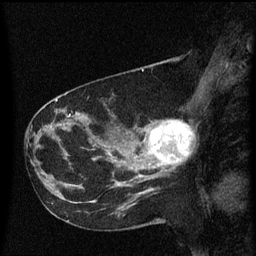
Breast MRI (dynamic contrast-enhanced), one sagittal slice; slice 26 of 60 in the series (ordered by position); dynamic contrast-enhanced series, image 2 of 3 at this slice position (ordered by acquisition); 1.5 T; TE 4.2 ms, TR 8.4 ms; 2 mm slice thickness; 256 × 256 image matrix. Female patient, age 41 years. Case-level facts recorded for this patient, not image findings: setting: breast cancer imaged before/during neoadjuvant chemotherapy; receptor status: triple-negative.
Annotated regions visible in this slice (semi-automatic segmentation, software-assisted and operator-edited):
- analysis volume of interest (the breast-tissue region the enhancement analysis was run in; not a lesion): bounding box (x1, y1, x2, y2) in pixels: (138, 120, 193, 177)
- tumour enhancement mask (voxels above the 70 % enhancement threshold inside the analysis volume of interest): (149, 120, 192, 165)